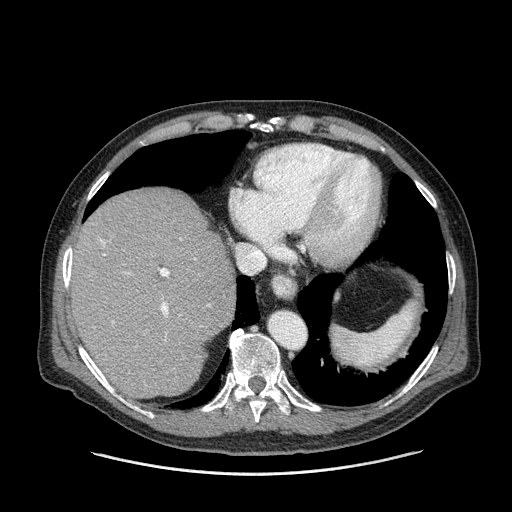
Contrast-enhanced abdominal CT (liver protocol), one axial slice; slice 120 of 180 in the series (ordered by position); reconstruction kernel STANDARD; one of 2 acquisitions stored at this slice position; soft-tissue window (W 400 / L 40 HU); 2.5 mm slice thickness; 512 × 512 image matrix, field of view 420 × 420 mm. Case-level facts recorded for this patient, not image findings: diagnosis: hepatocellular carcinoma (patient treated with transarterial chemoembolisation; whether this scan precedes or follows treatment is not stated here); TNM stage (as recorded): Stage-II; Child-Pugh class: A; tumour differentiation: well differentiated; tumour nodularity: multinodular.
Annotated regions visible in this slice (semi-automatically segmented with operator editing):
- liver parenchyma outside the tumour (the mass and vessels are separate outlines, so this box may not span the whole liver): bounding box <72,190,234,398> (left, top, right, bottom; pixels)
- liver vessels: <100,238,209,323>